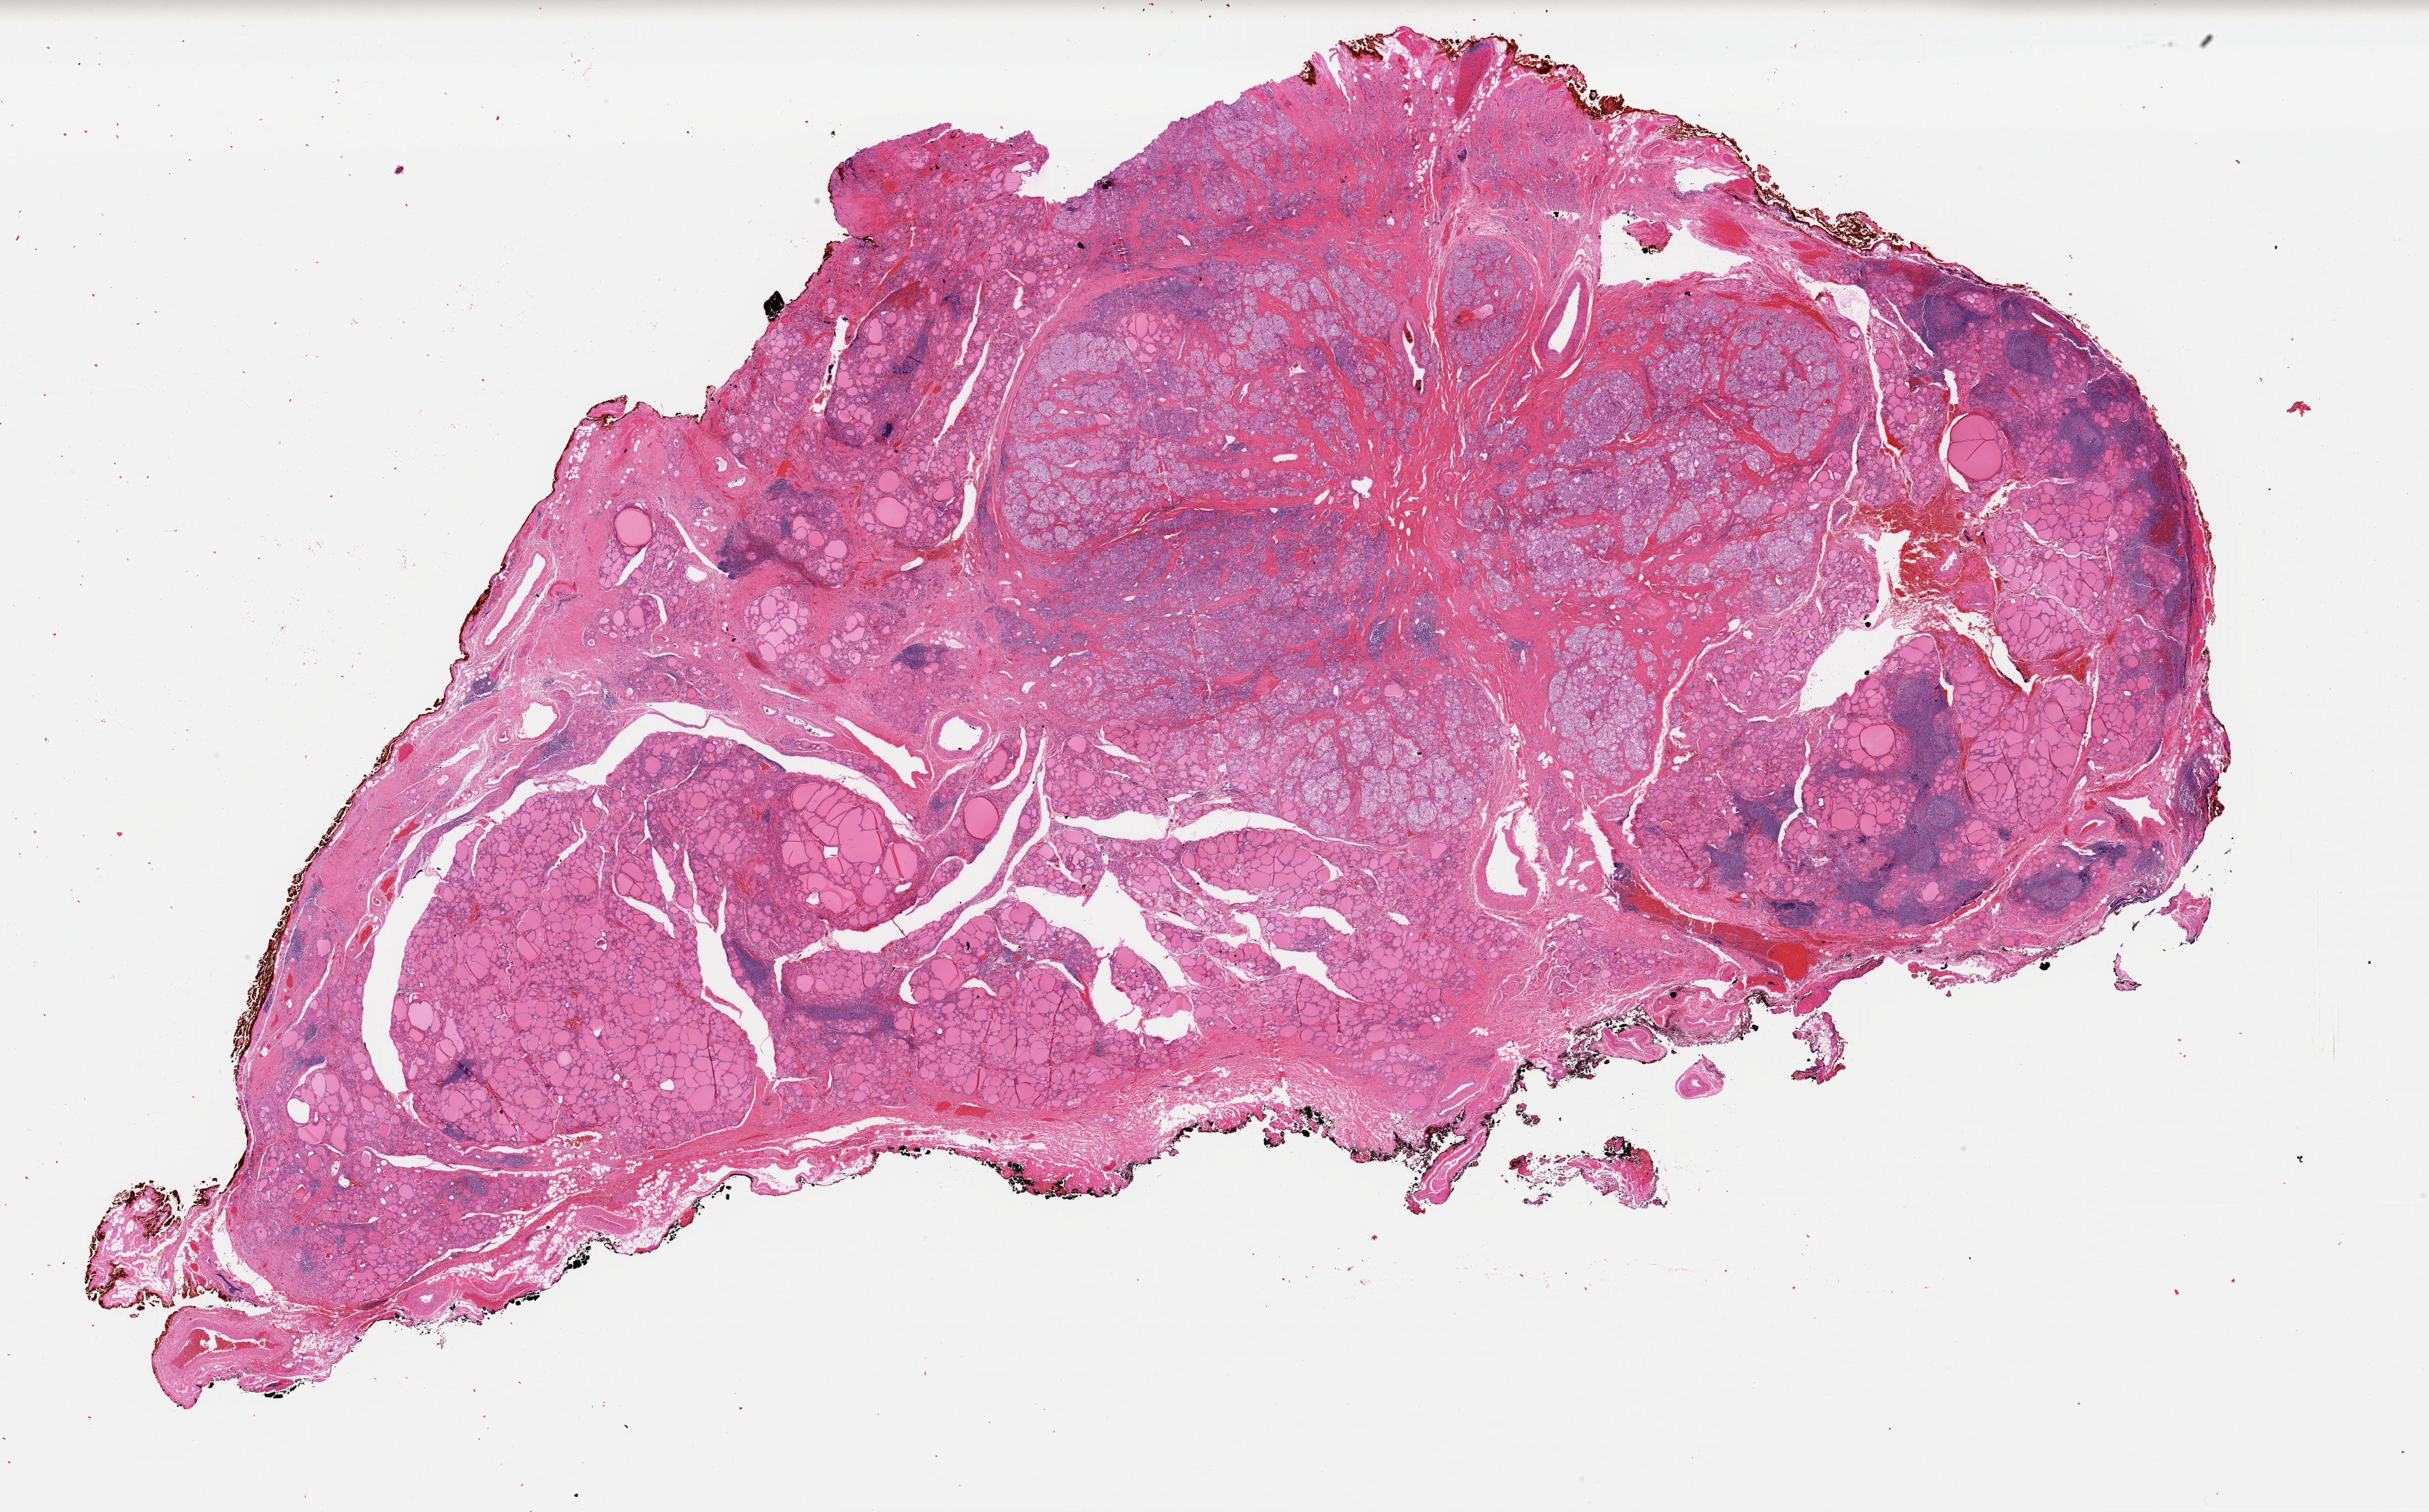
Whole-slide histology image, Hematoxylin and eosin (H&E) stained — a low-resolution overview of the entire scanned area, about 28.0 x 17.4 mm; FFPE section; sample: primary tumour, thyroid. Female, age 43 years at initial diagnosis.
Laterality: right. AJCC pathologic stage: I (6th edition). Lymph nodes positive (case pathology): 0 of 2 examined. Diagnosis: Papillary carcinoma, follicular variant (thyroid gland).